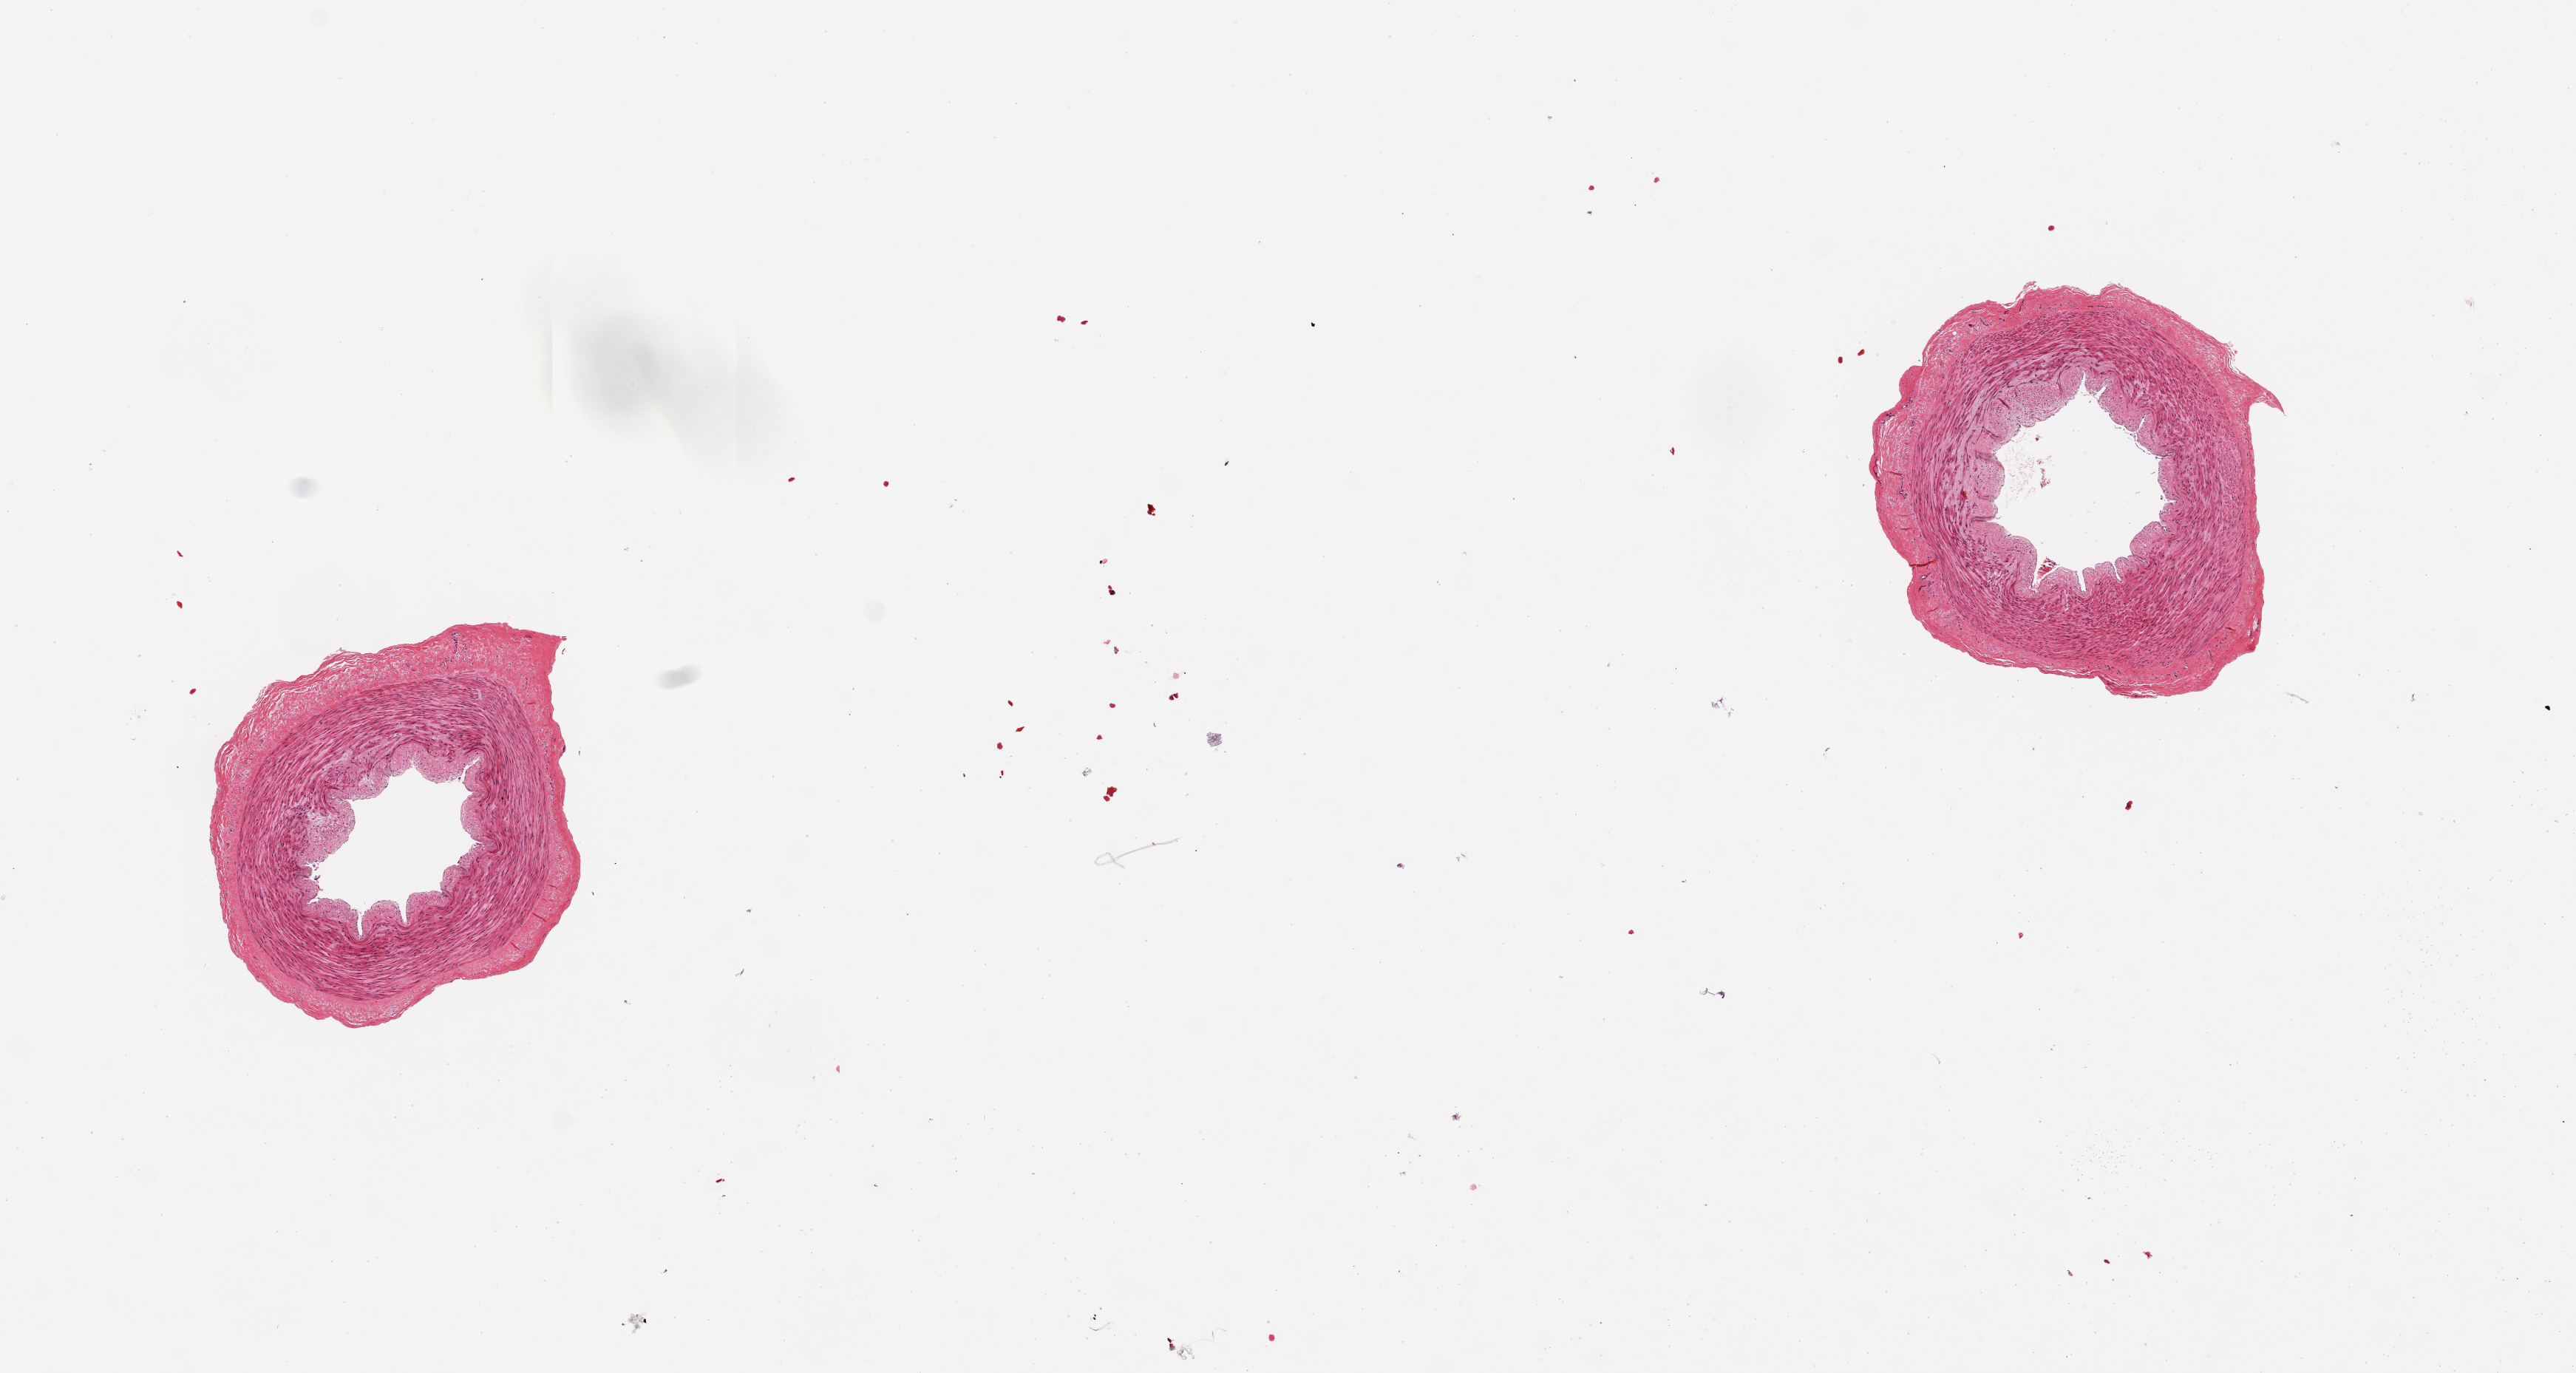
H&E whole-slide image, a low-resolution overview of the entire scanned area, about 13.8 x 7.3 mm (slide scanned at 20x). PAXgene-fixed, paraffin-embedded tissue. Target tissue: tibial artery. Donor tissue sample.
Review note (as recorded): 2 pieces; well trimmed.